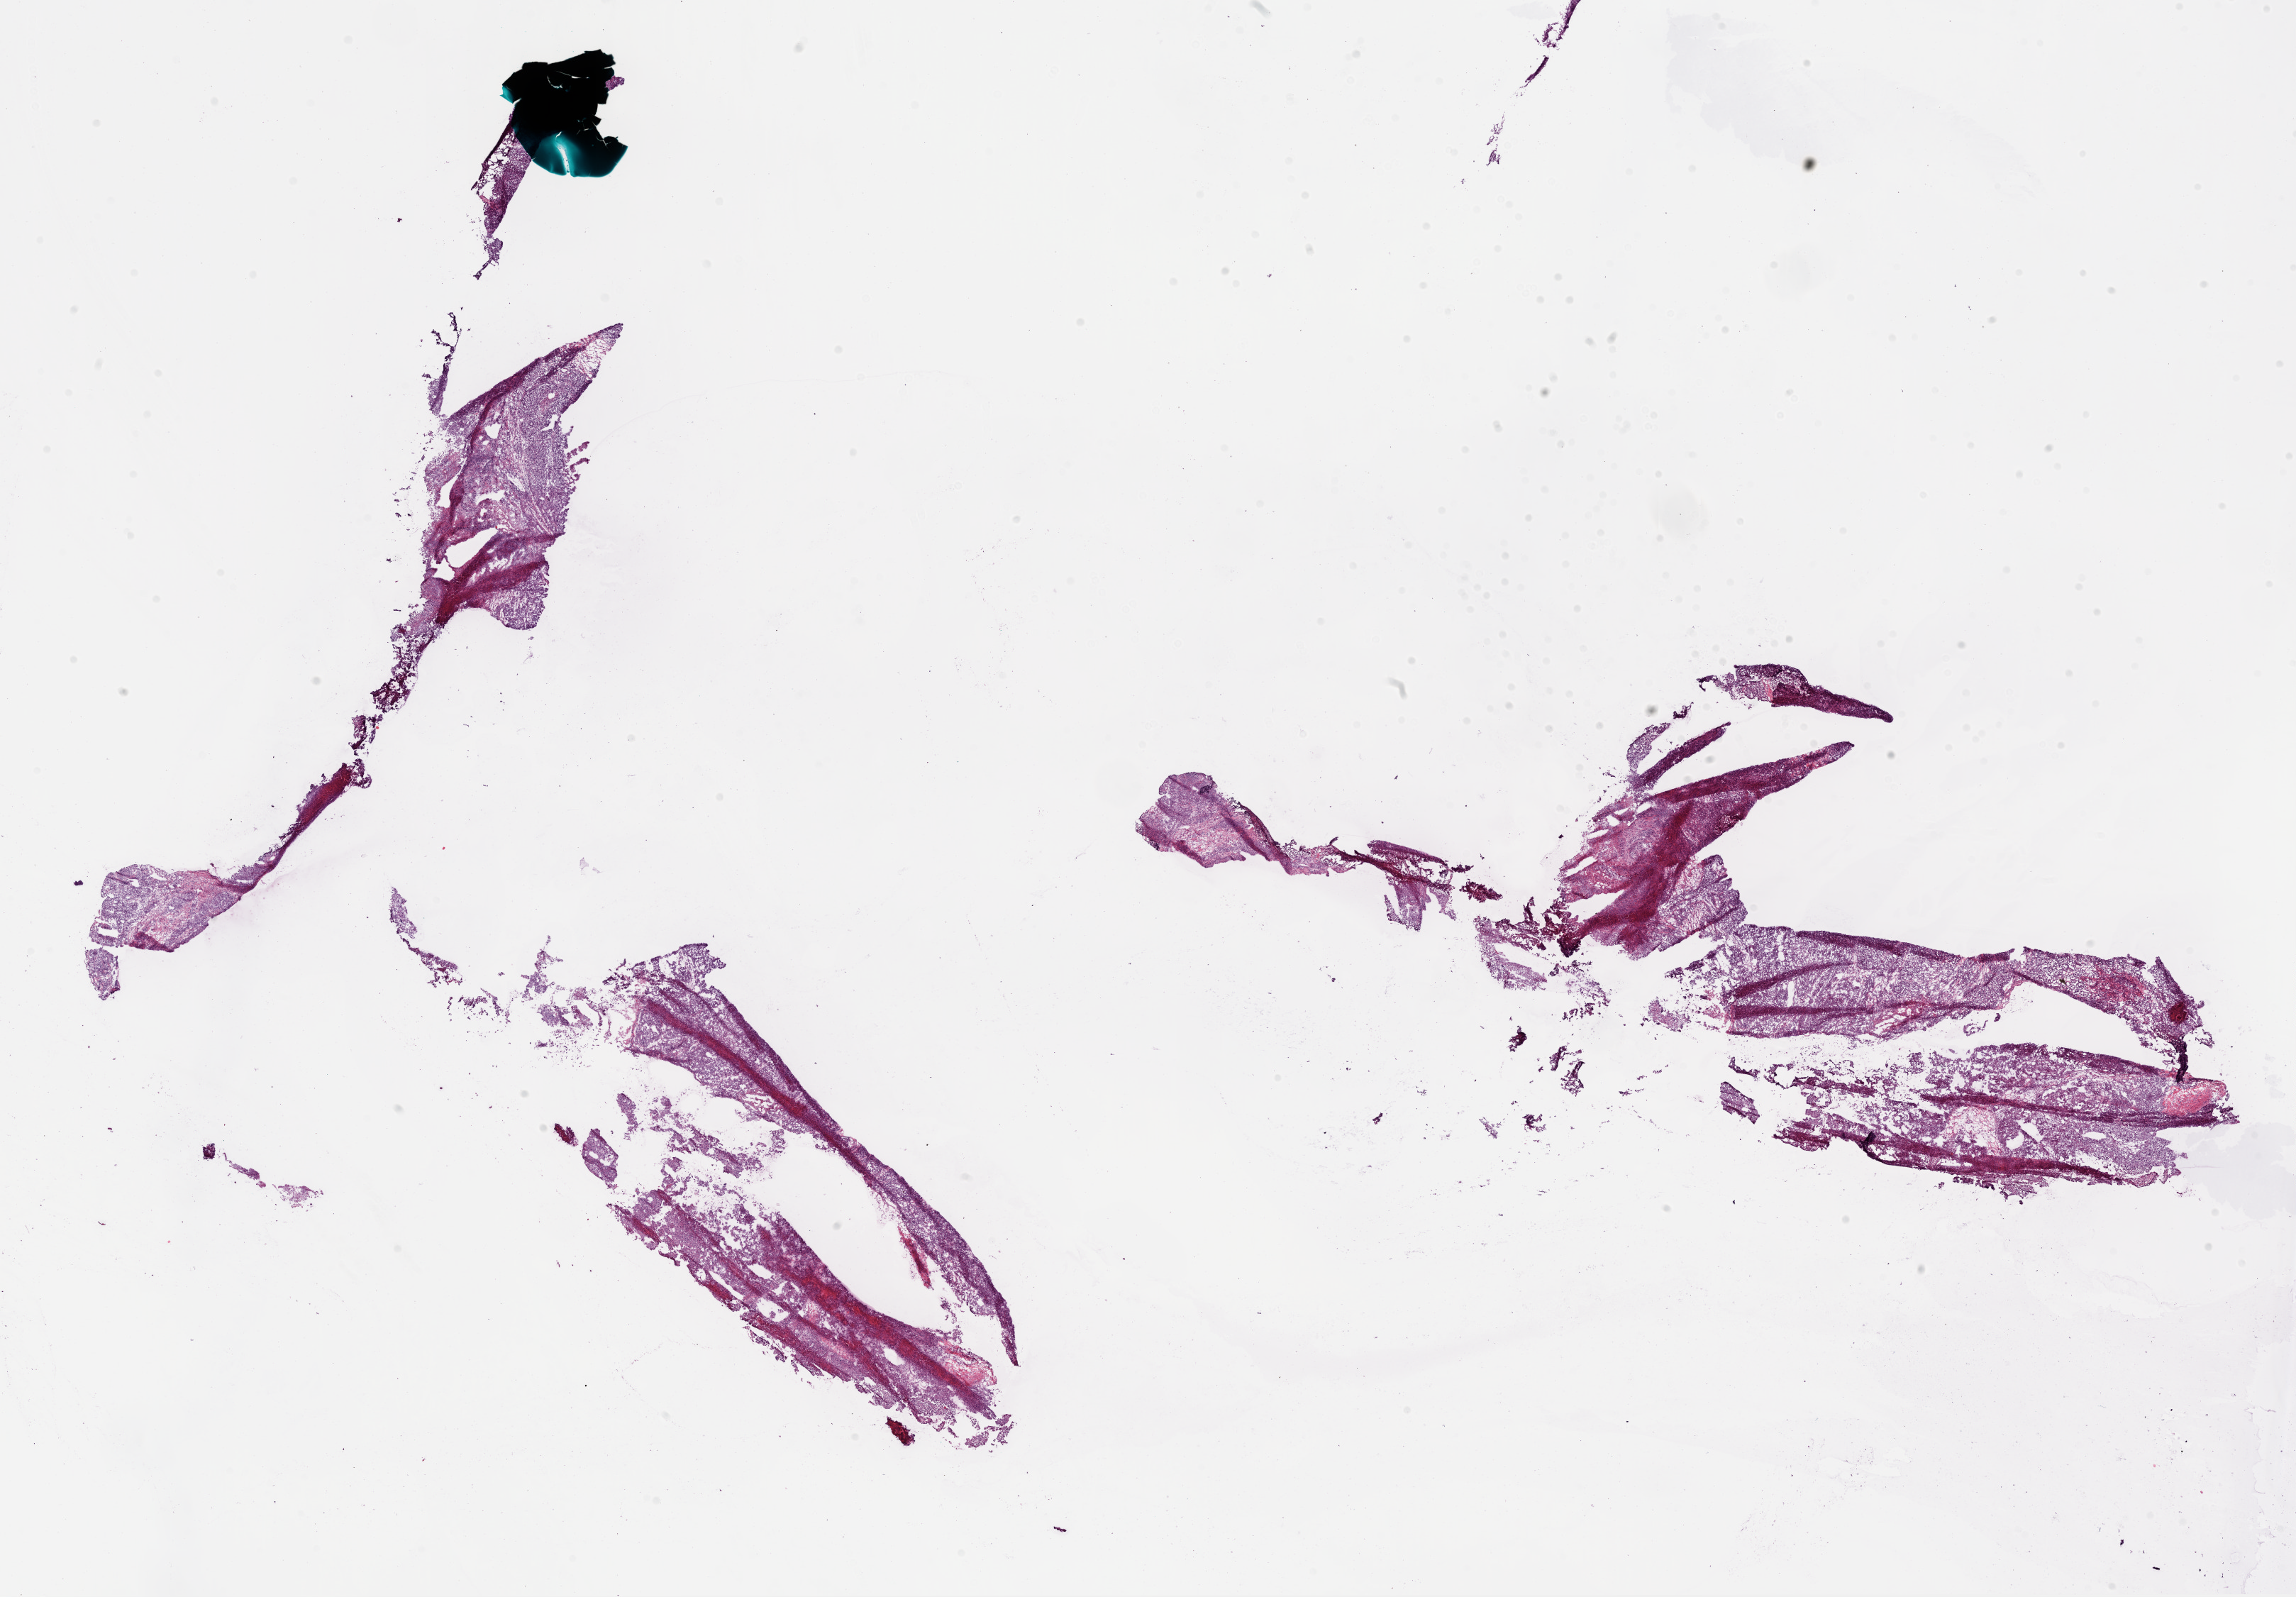
Digitized H&E-stained tissue section (whole slide), a low-resolution overview of the entire scanned area, about 26.1 x 18.2 mm (slide scanned at 20x), frozen section from the bottom of the tissue portion, primary tumour sample from the ovary. Female patient; age at initial diagnosis 61 years. Histologic grade: G3 (poorly differentiated). Slide review estimates, as recorded: tumour cells 65%, tumour nuclei 90%, normal cells 15%, stromal cells 0%, necrosis 20%.
Laterality: bilateral. FIGO stage: IIIC. Pathologic diagnosis: Serous cystadenocarcinoma, NOS.